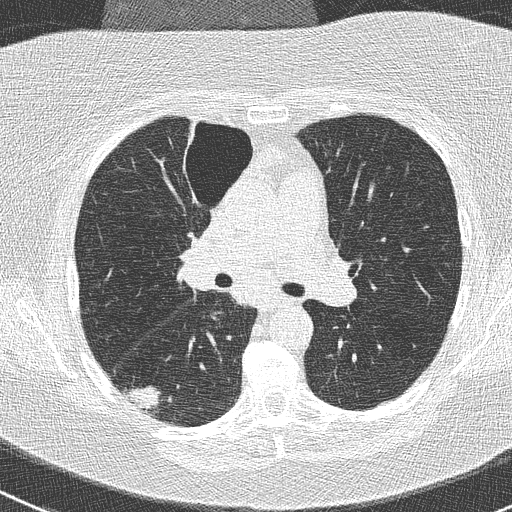
Low-dose screening chest CT, axial slice. Baseline screening round. Lung window (W 1500 / L -600 HU). Lung (sharp) reconstruction kernel (B50f). Slice 104 of 261 in the series. Female, age 74 years at enrolment. Former smoker at enrolment.
Lesion marked by an expert reader, box from (x=115, y=378) to (x=173, y=423) px. The screening reader recorded 3 non-calcified nodules or masses ≥4 mm on this exam (right lower lobe, right upper lobe, left lower lobe); which of them this box marks is not recorded. Participant outcome: lung cancer diagnosed 16 days after this screen — non-small cell carcinoma, right lower lobe, poorly differentiated (G3), stage IIIA (AJCC 6th edition), 28 mm at pathology.